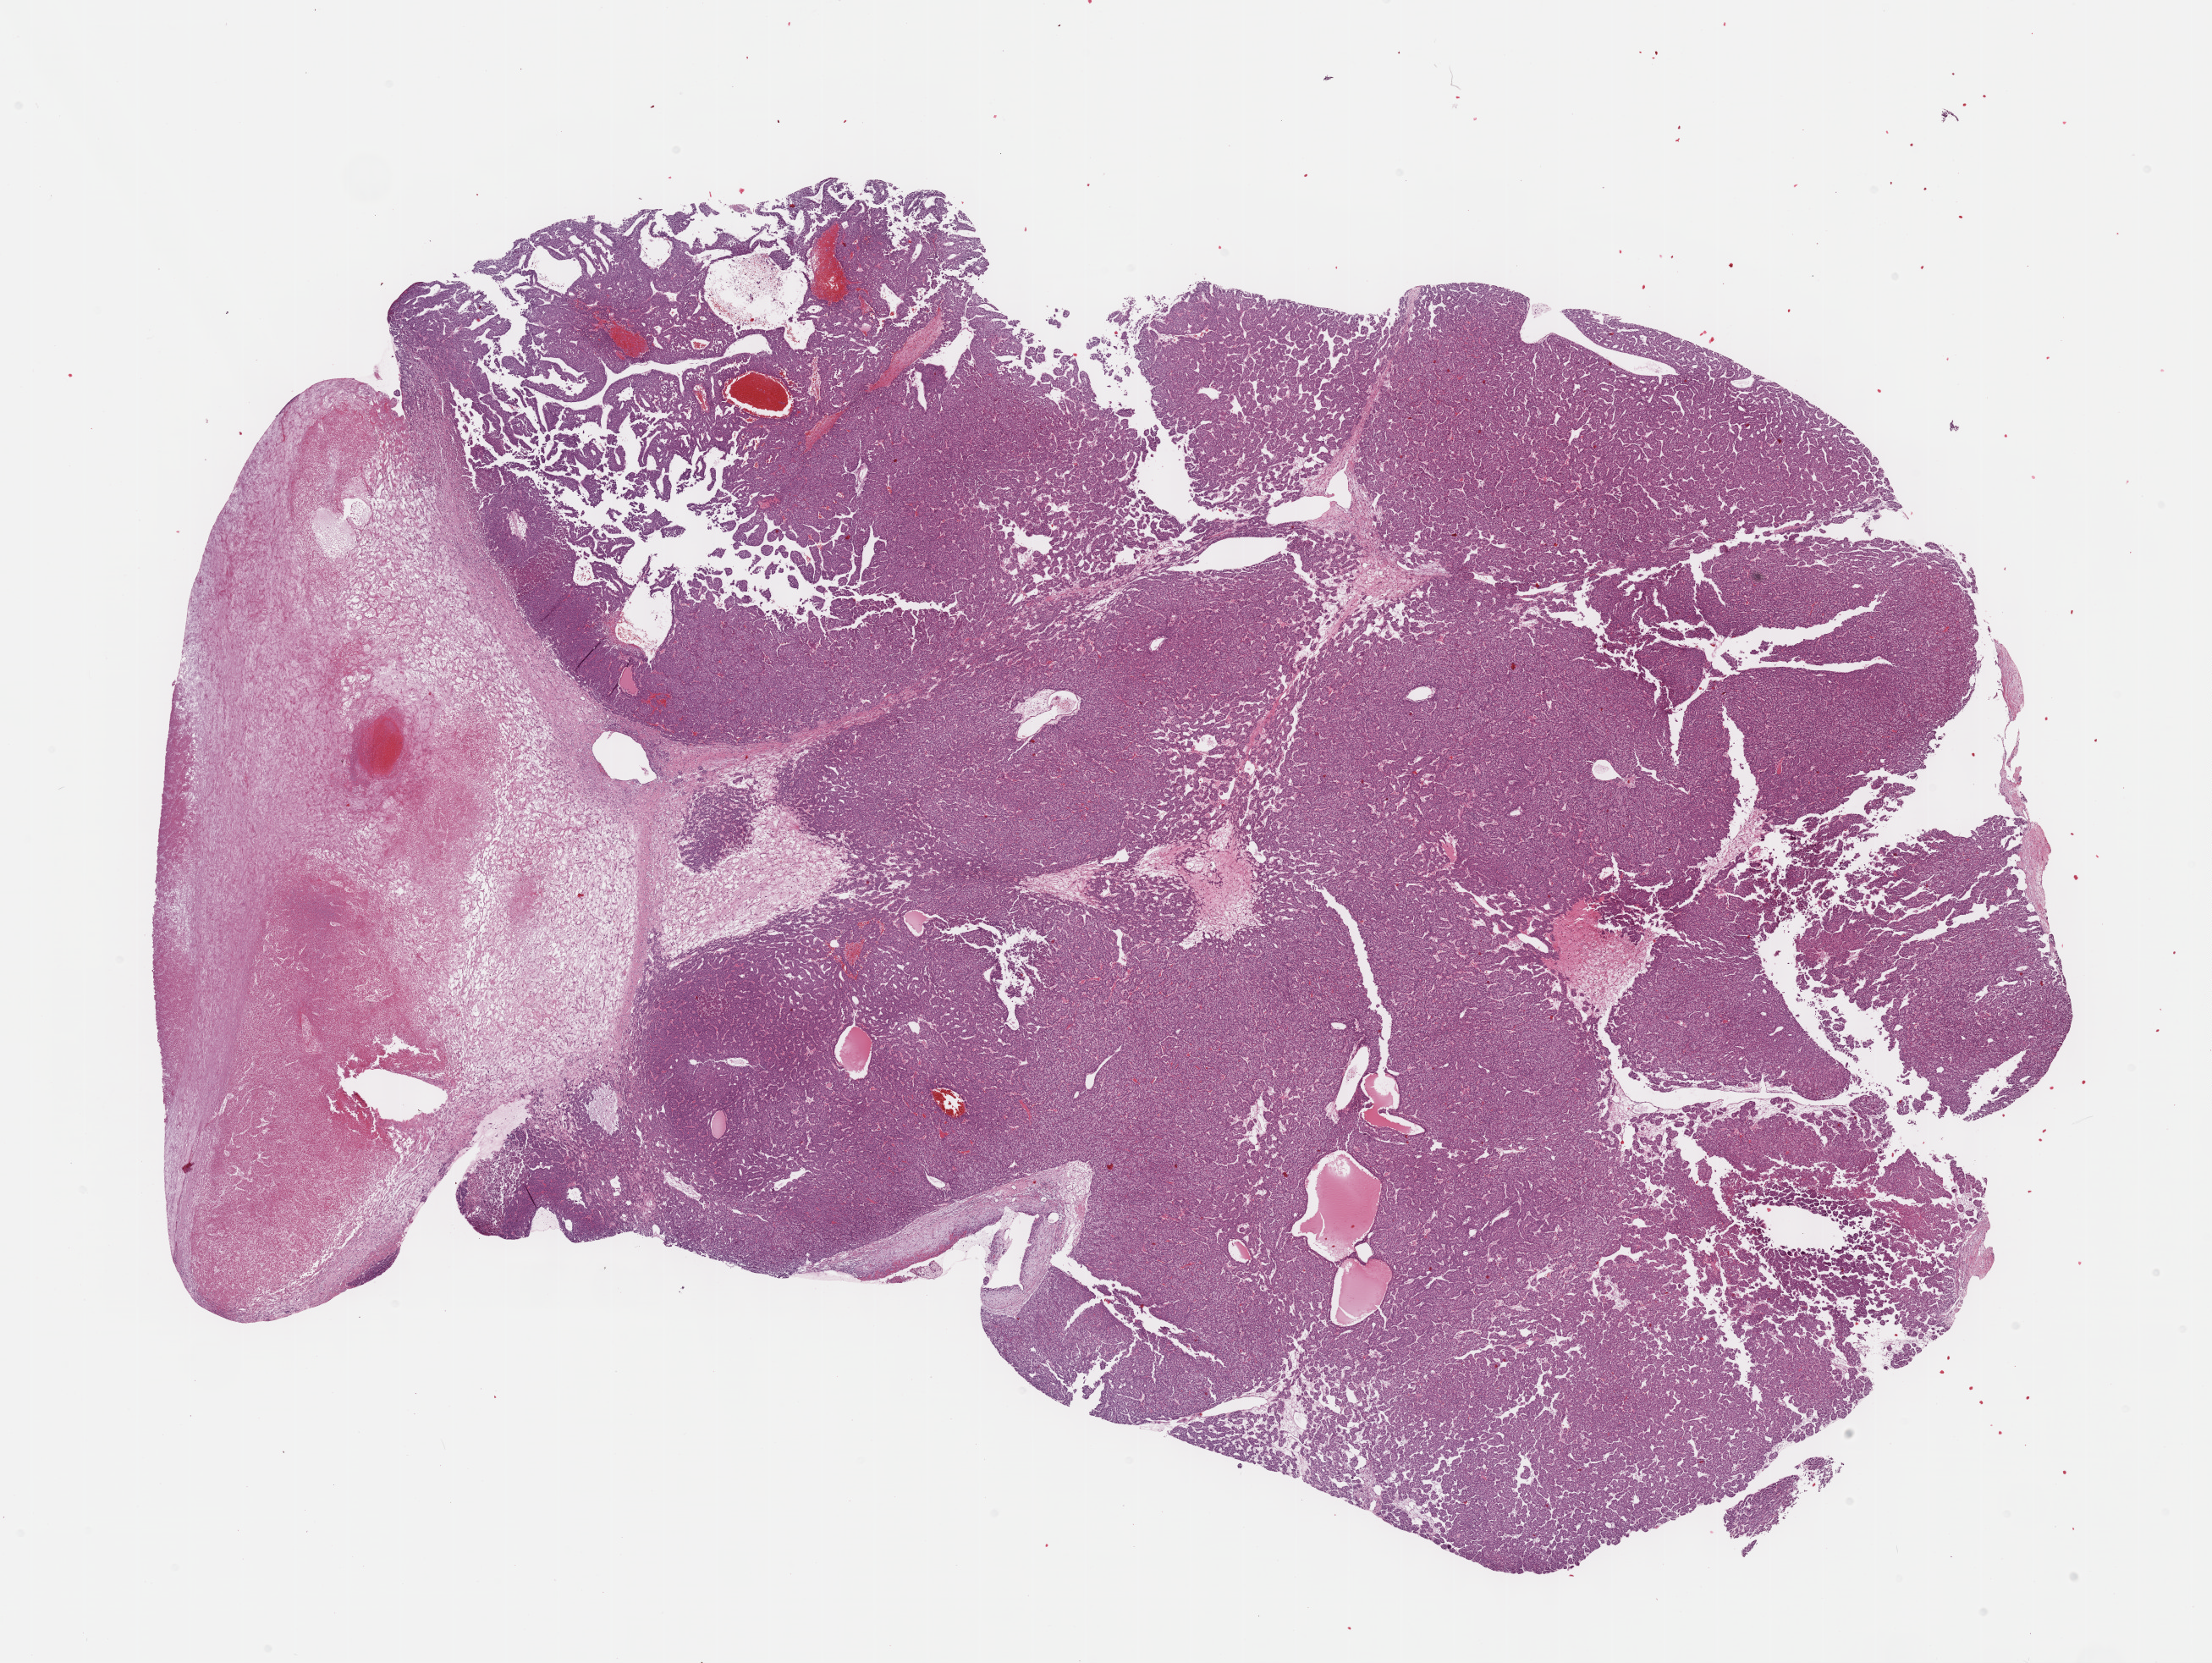
Digitized H&E-stained tissue section (whole slide), low-resolution overview of the scanned area, about 21.1 x 15.9 mm; FFPE section; liver, primary tumour sample. Female patient; age at initial diagnosis 43 years. Histologic grade: G2 (moderately differentiated).
AJCC pathologic stage: II (4th edition). Diagnosis: Hepatocellular carcinoma, NOS.